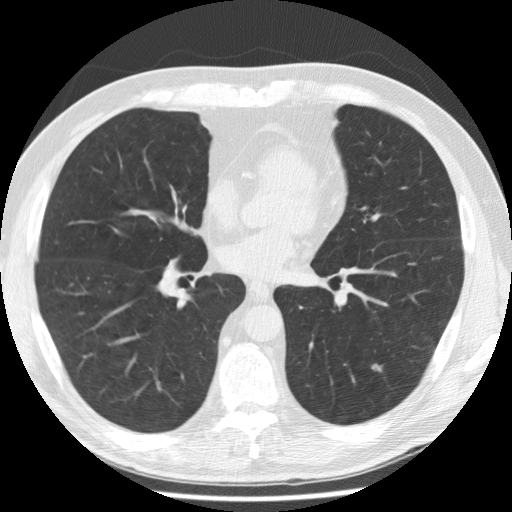
Chest CT (low-dose screening protocol), one axial image, second annual screen, lung window (W 1500 / L -600 HU), 2.5 mm slice thickness, 512 × 512 image matrix, field of view 350 × 350 mm. Male participant, aged 58 years at enrolment.
• Expert-annotated lung lesion, box from (x=357, y=352) to (x=395, y=384) px.
• The exam's reader record, not a measurement of the box and not confirmed to be the same lesion: non-calcified nodule or mass ≥4 mm, left lower lobe, 7 × 4 mm, poorly defined margins, ground glass attenuation, pre-existing on the prior screen: yes; interval growth: yes.
• Official screen result: positive, change unspecified: nodule(s) >= 4 mm or enlarging nodule(s), mass(es), or other non-specific abnormalities suspicious for lung cancer.